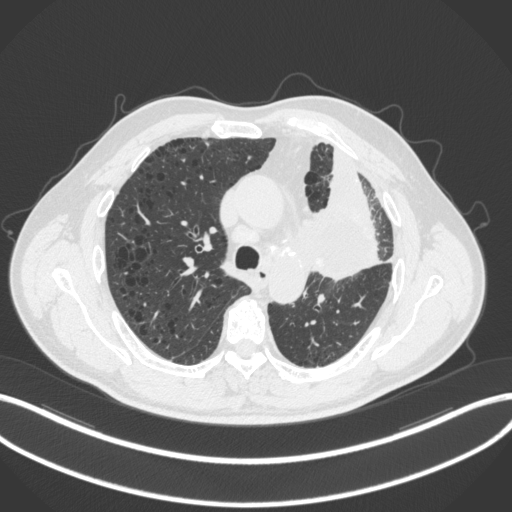
Chest CT, one axial slice. Position 199 of 286 along the scan axis. Reconstruction kernel B31f. Lung window (W 1500 / L -600 HU). 1 mm slice thickness. 512 × 512 image matrix, field of view 400 × 400 mm. Patient: male, 68 years. From the clinical record (not read from this slice): clinical TNM (as recorded): T3 N3 M1.
Structures marked on this image (rectangle marked by the reading radiologist):
- lung tumour (recorded histology: adenocarcinoma): box from (x=297, y=198) to (x=379, y=286) px